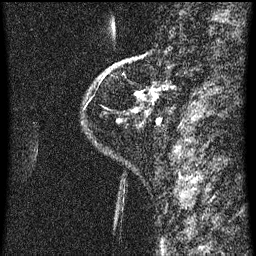
Breast MRI (dynamic contrast-enhanced), one sagittal slice. Dynamic contrast-enhanced series, image 2 of 3 at this slice position (ordered by acquisition). 1.5 T. TE 4.2 ms, TR 8 ms. 2 mm slice thickness. 256 × 256 image matrix. Female patient, age 48 years.
Structures marked on this image (semi-automatically segmented with operator editing):
- analysis volume of interest (the breast-tissue region the enhancement analysis was run in; not a lesion): bounding box [x1, y1, x2, y2] px = [128, 54, 174, 125]
- tumour enhancement mask (voxels above the 70 % enhancement threshold inside the analysis volume of interest): [132, 90, 162, 125]